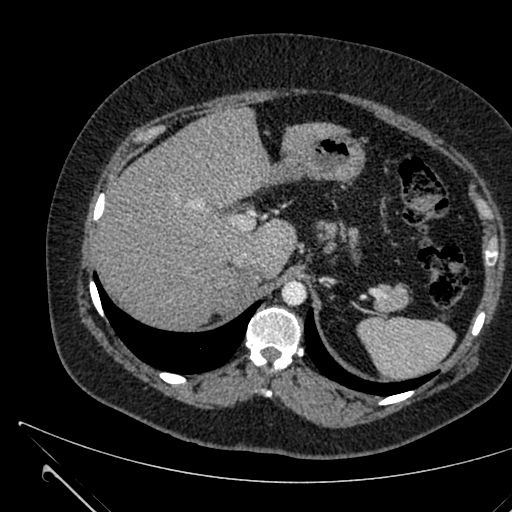
Contrast-enhanced abdominal CT, one axial slice; slice 481 of 731 in the series (ordered by position); intravenous contrast given; soft-tissue window (W 400 / L 40 HU); 512 × 512 image matrix, field of view 376 × 376 mm. Patient: female, 36 years. Case-level facts recorded for this patient, not image findings: diagnosis: adrenocortical carcinoma; tumour side: right adrenal; tumour size at pathology: 10 cm; Ki-67 index: 20 %; stage (as recorded): 4.
Structures marked on this image (semi-automatically segmented with operator editing):
- mass: box from (x=215, y=266) to (x=260, y=312) px